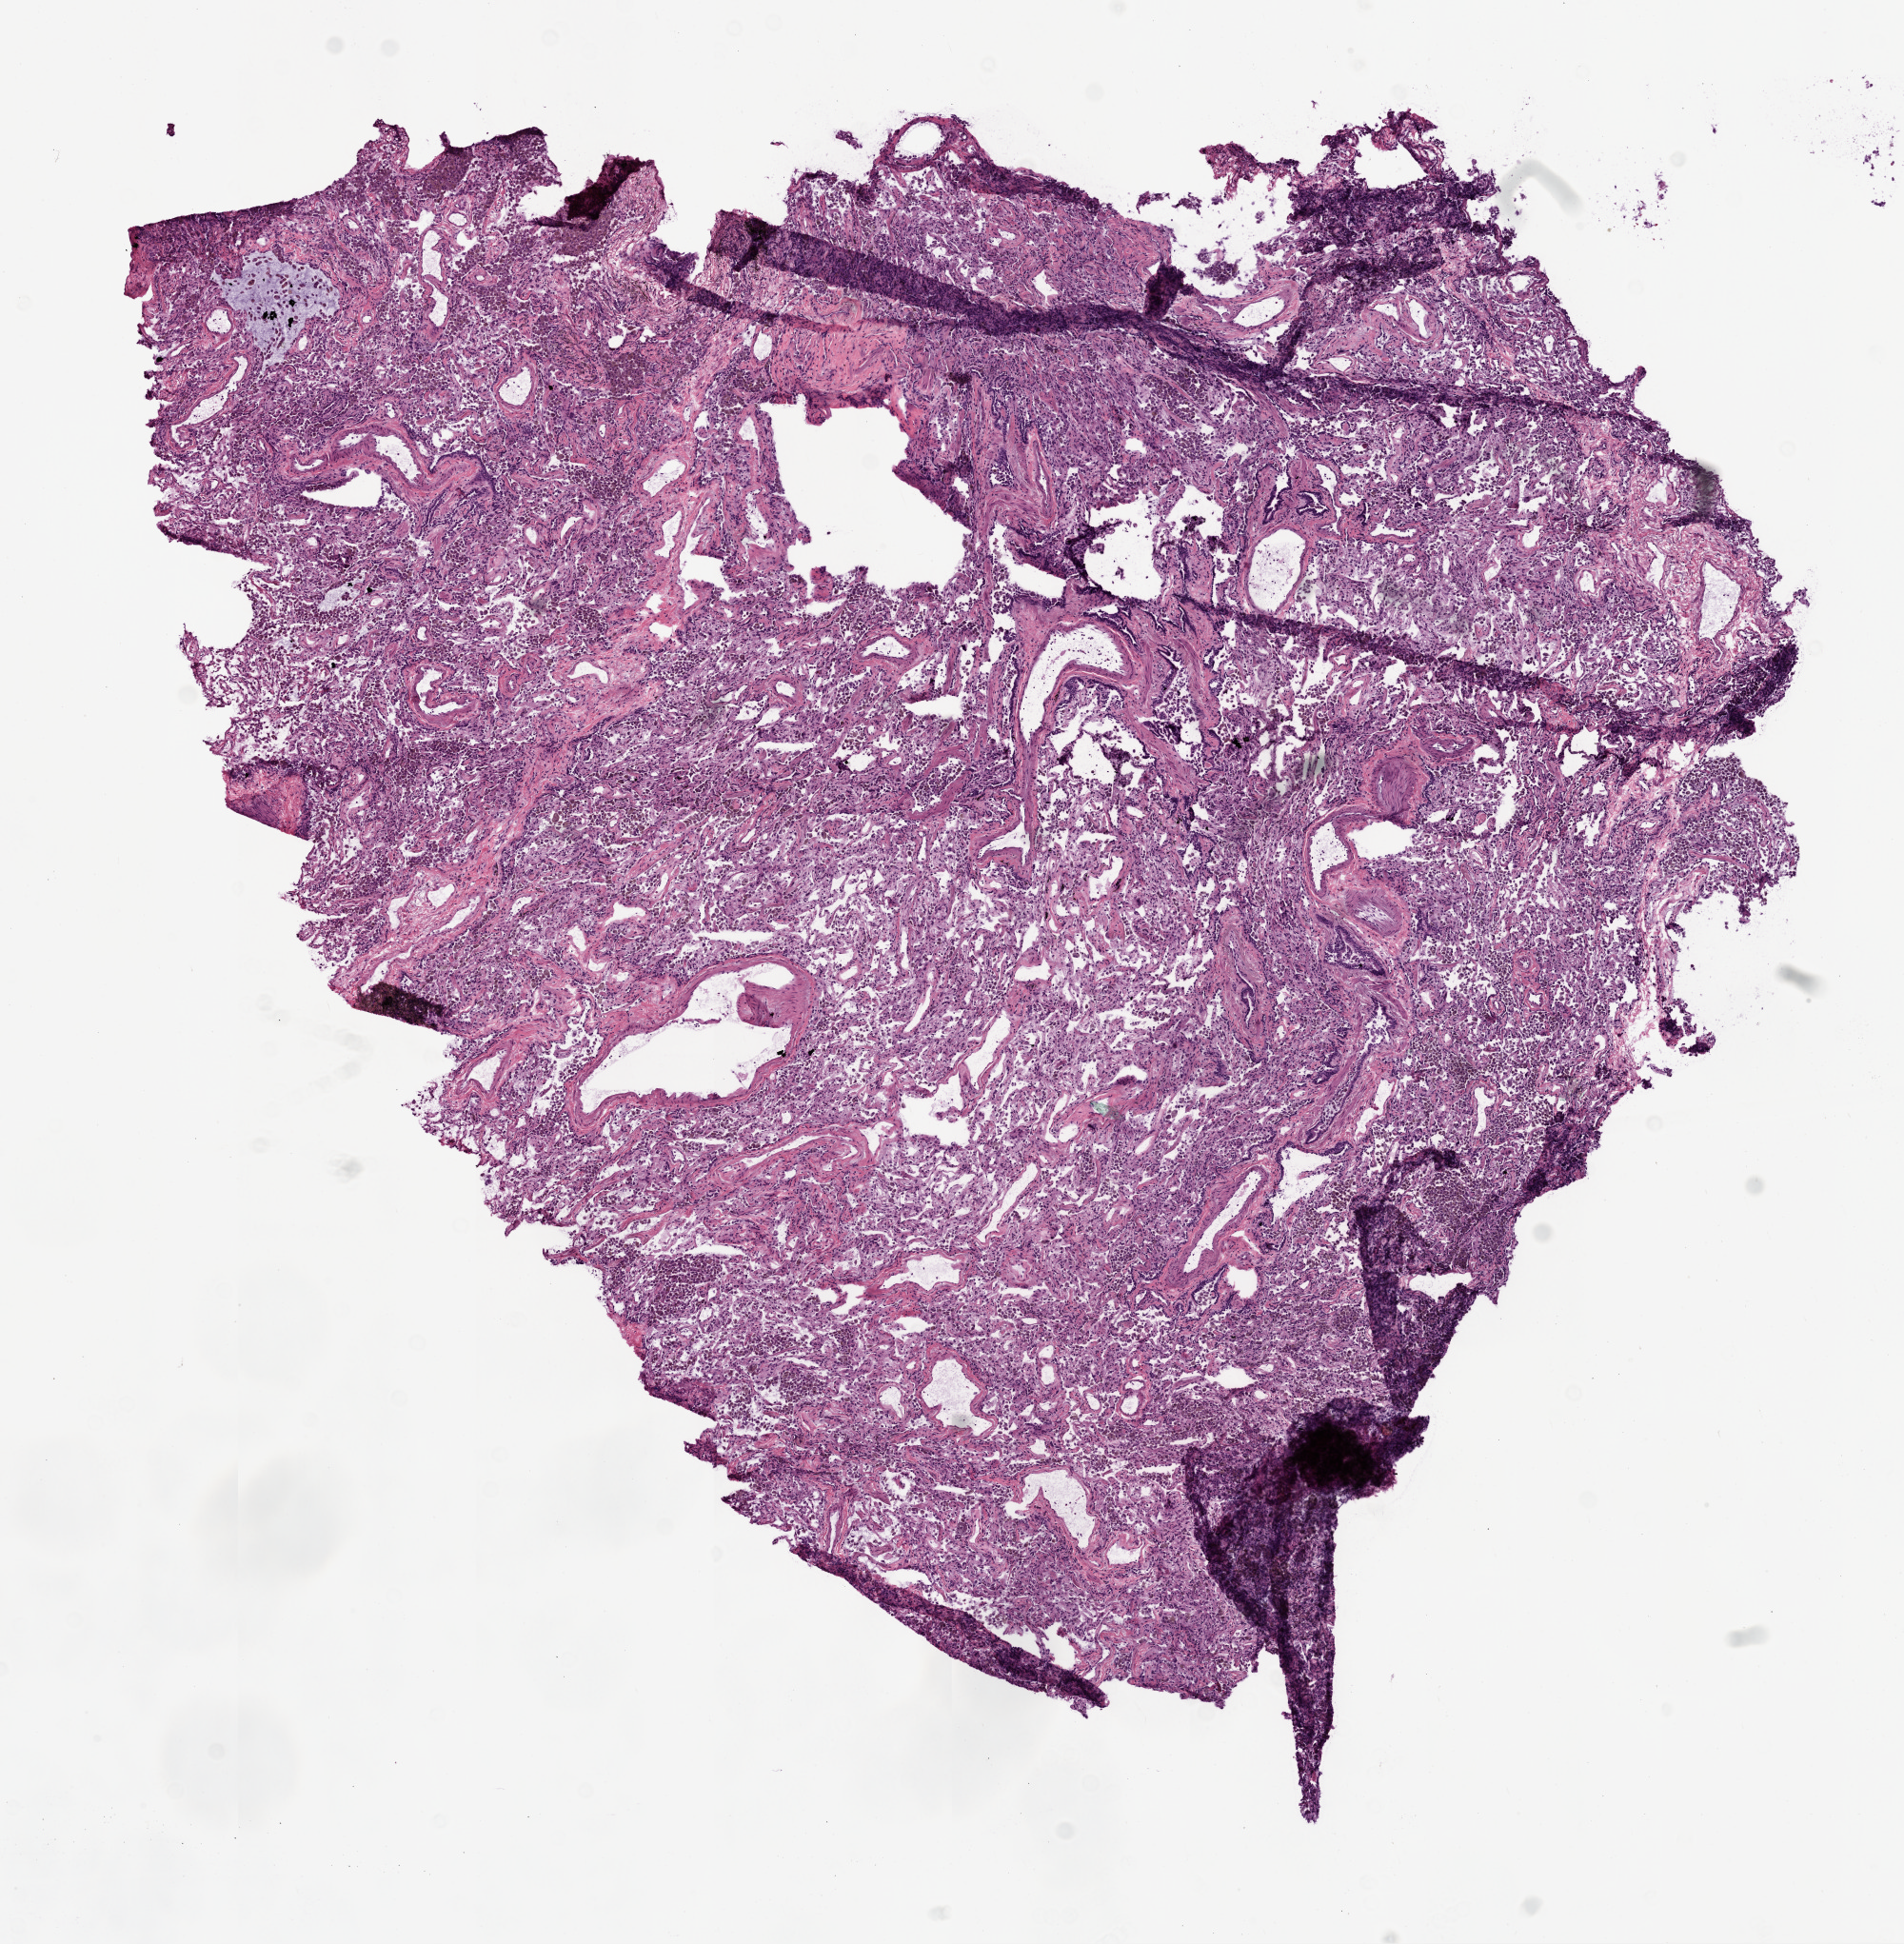
Whole-slide histology image, Hematoxylin and eosin (H&E) stained, whole scanned area (about 8.0 x 8.2 mm, from a 20x scan) shown as a low-resolution overview. Frozen section. Solid tissue normal (non-tumour tissue) sample from the lung. Patient: female, age at initial diagnosis 64 years.
This section: solid tissue normal sample (biorepository sample class). Patient diagnosis: Squamous cell carcinoma, NOS.